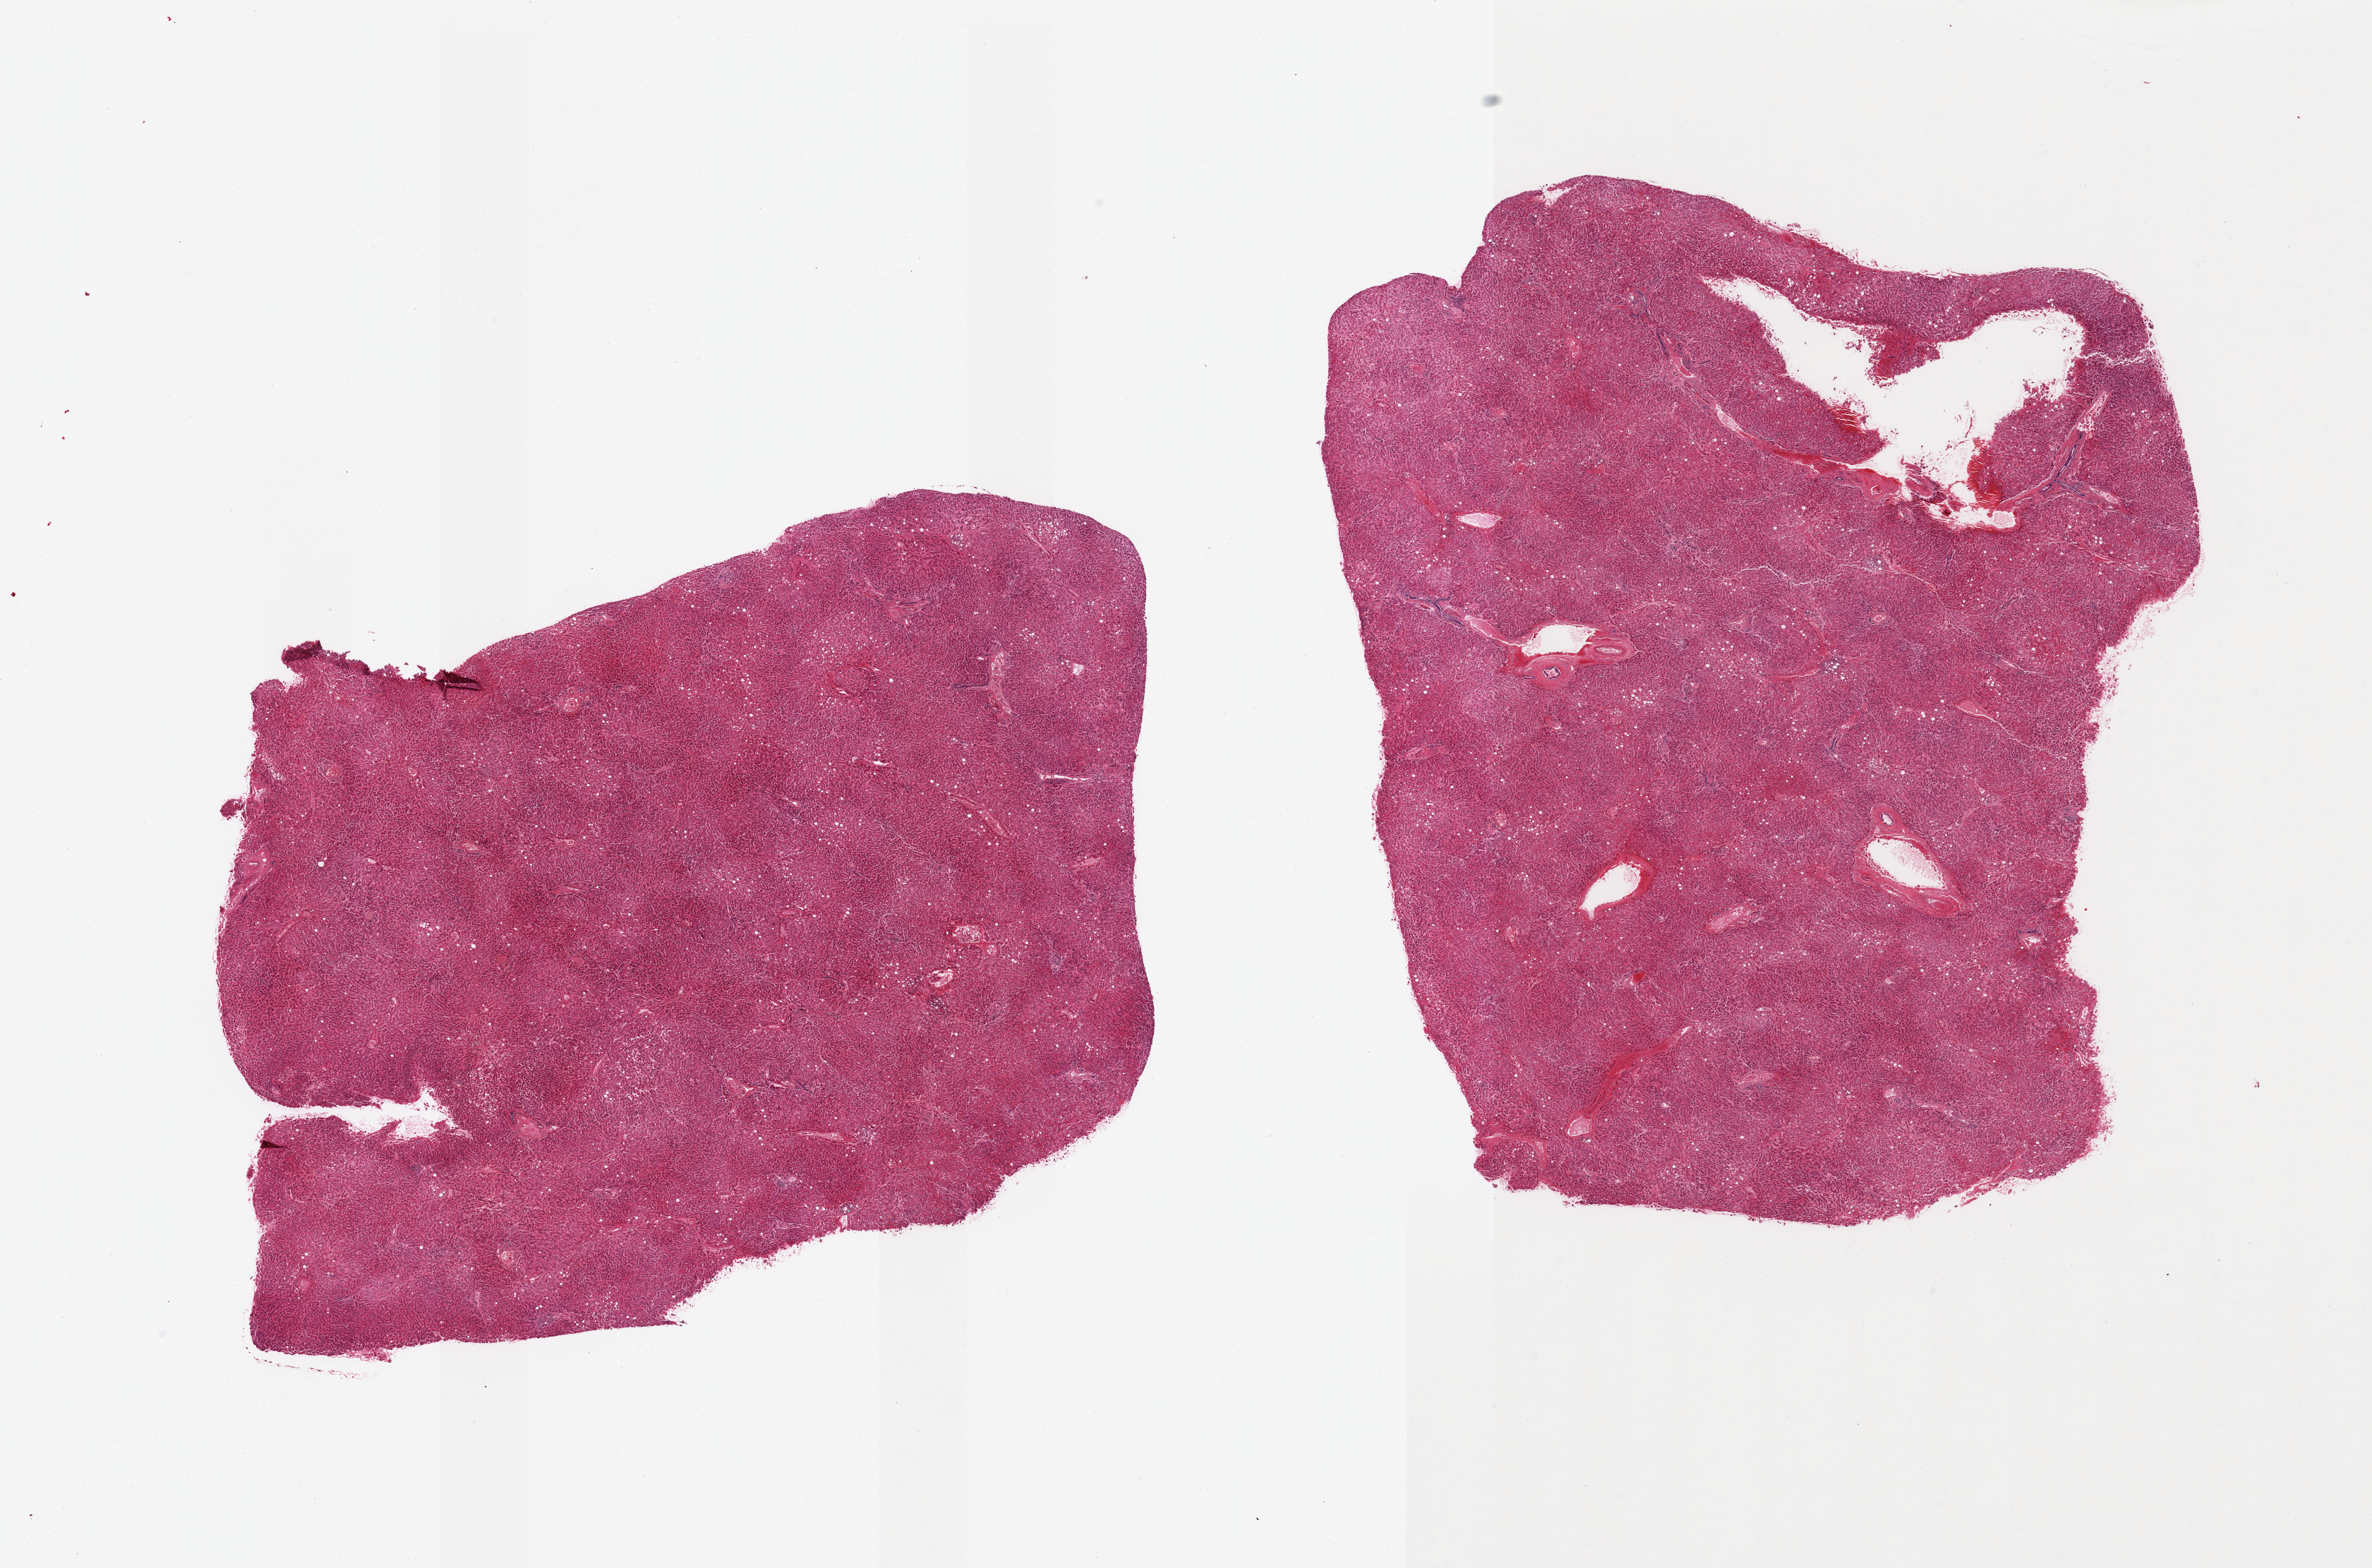
Hematoxylin and eosin (H&E) whole-slide image — shown as a low-resolution overview of the whole scanned area (about 26.6 x 17.6 mm), PAXgene-fixed paraffin-embedded (PFPE) section, target tissue: liver, tissue donor sample. Male donor.
- reviewer comment on this tissue sample: 2 pieces; marked congestion; mild to moderate fatty degeneration